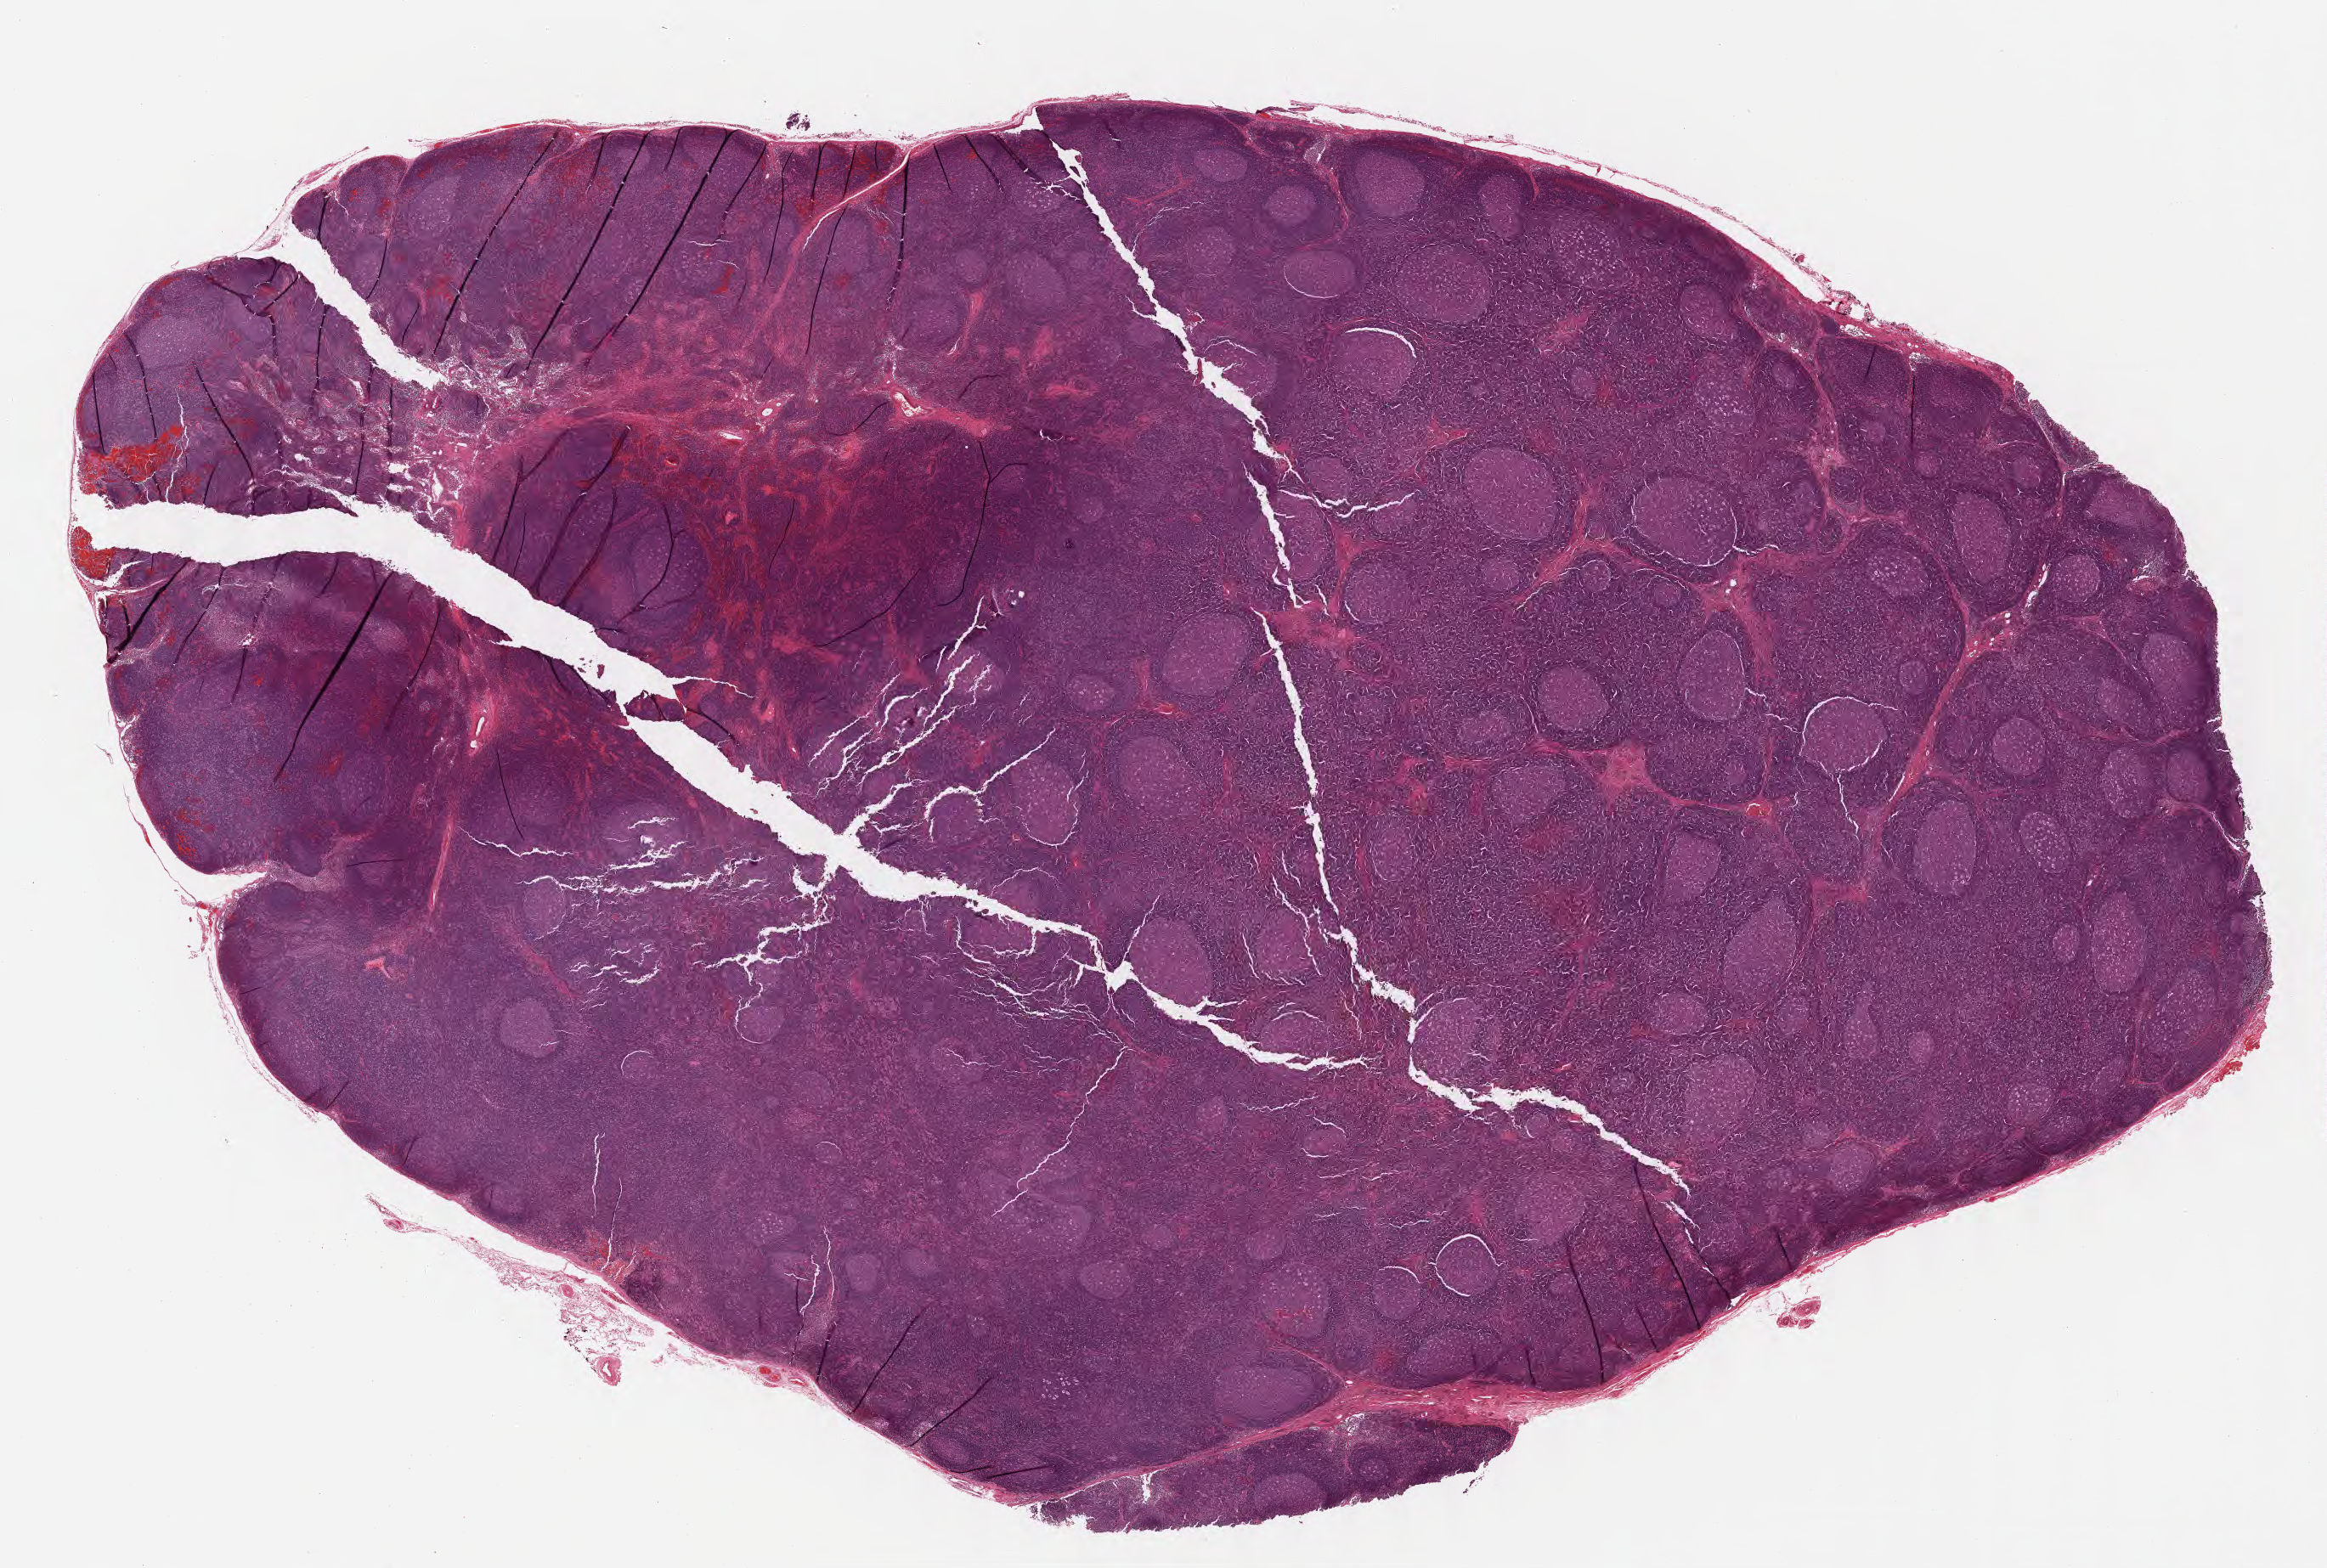
Whole-slide image, hematoxylin and eosin (H&E) stain — whole scanned area (about 22.1 x 14.9 mm) shown as a low-resolution overview. Formalin-fixed paraffin-embedded section. Specimen: normal-tissue sample (non-tumor) from a patient with burkitt lymphoma, NOS. Male patient; age at initial diagnosis 4 years. Slide review estimates, as recorded: tumor cells 0%, tumor nuclei 0%, stromal cells 0%, necrosis 0%, normal cells 100%. Inflammatory infiltration, as recorded: lymphocyte infiltration 90%, monocyte infiltration 5%, neutrophil infiltration 0%.
This section: non-tumor tissue sample; the patient's diagnosis is given above.